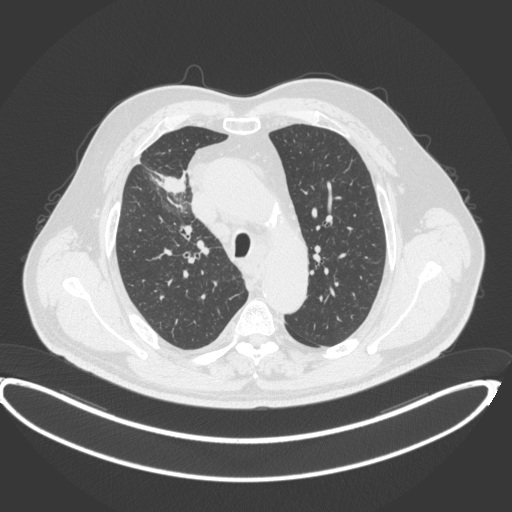
Chest CT, one axial slice; slice 298 of 395 in the series (ordered by position); reconstruction kernel B31f; 120 kVp; lung window (W 1500 / L -600 HU); 512 × 512 image matrix. Male patient, age 62 years. From the clinical record (not read from this slice): clinical TNM (as recorded): T1c N3 M1c.
Structures marked on this image (rectangle marked by the reading radiologist):
- lung tumour (recorded histology: adenocarcinoma): bounding box [x1, y1, x2, y2] px = [154, 170, 187, 197]